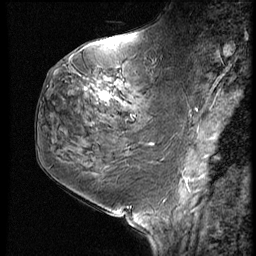
Breast MRI (dynamic contrast-enhanced), one sagittal slice. Position 27 of 60 along the scan axis. 3 images stored at this slice position (order not interpretable as contrast timing). 1.5 T. TE 4.2 ms, TR 9 ms. 2.5 mm slice thickness. 256 × 256 image matrix, field of view 180 × 180 mm. Female patient, age 59 years. Case-level facts recorded for this patient, not image findings: setting: breast cancer imaged before/during neoadjuvant chemotherapy; receptor status: HER2-positive.
Annotated regions visible in this slice (semi-automatically segmented with operator editing):
- analysis volume of interest (the breast-tissue region the enhancement analysis was run in; not a lesion): bounding box [x1, y1, x2, y2] px = [78, 61, 161, 125]
- tumour enhancement mask (voxels above the 140 % enhancement threshold inside the analysis volume of interest): [101, 93, 111, 102]